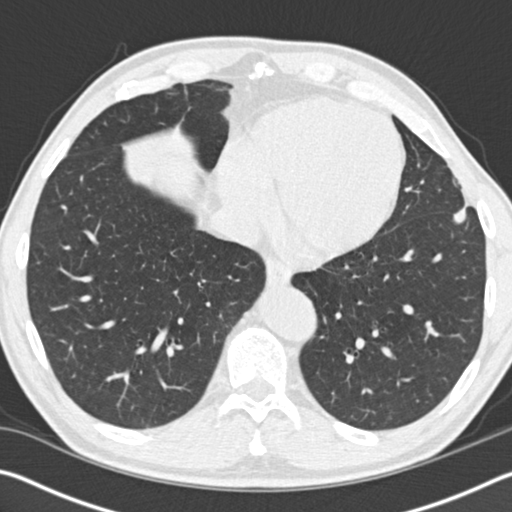
Low-dose screening chest CT, one axial slice. Slice 45 of 162 in the series (ordered by position). Lung window (W 1500 / L -600 HU). 512 × 512 image matrix.
Annotated regions visible in this slice (outlined manually by an expert reader):
- lesion 1 (tumor, upper lobe of left lung): bounding box <453,188,471,224> (left, top, right, bottom; pixels)